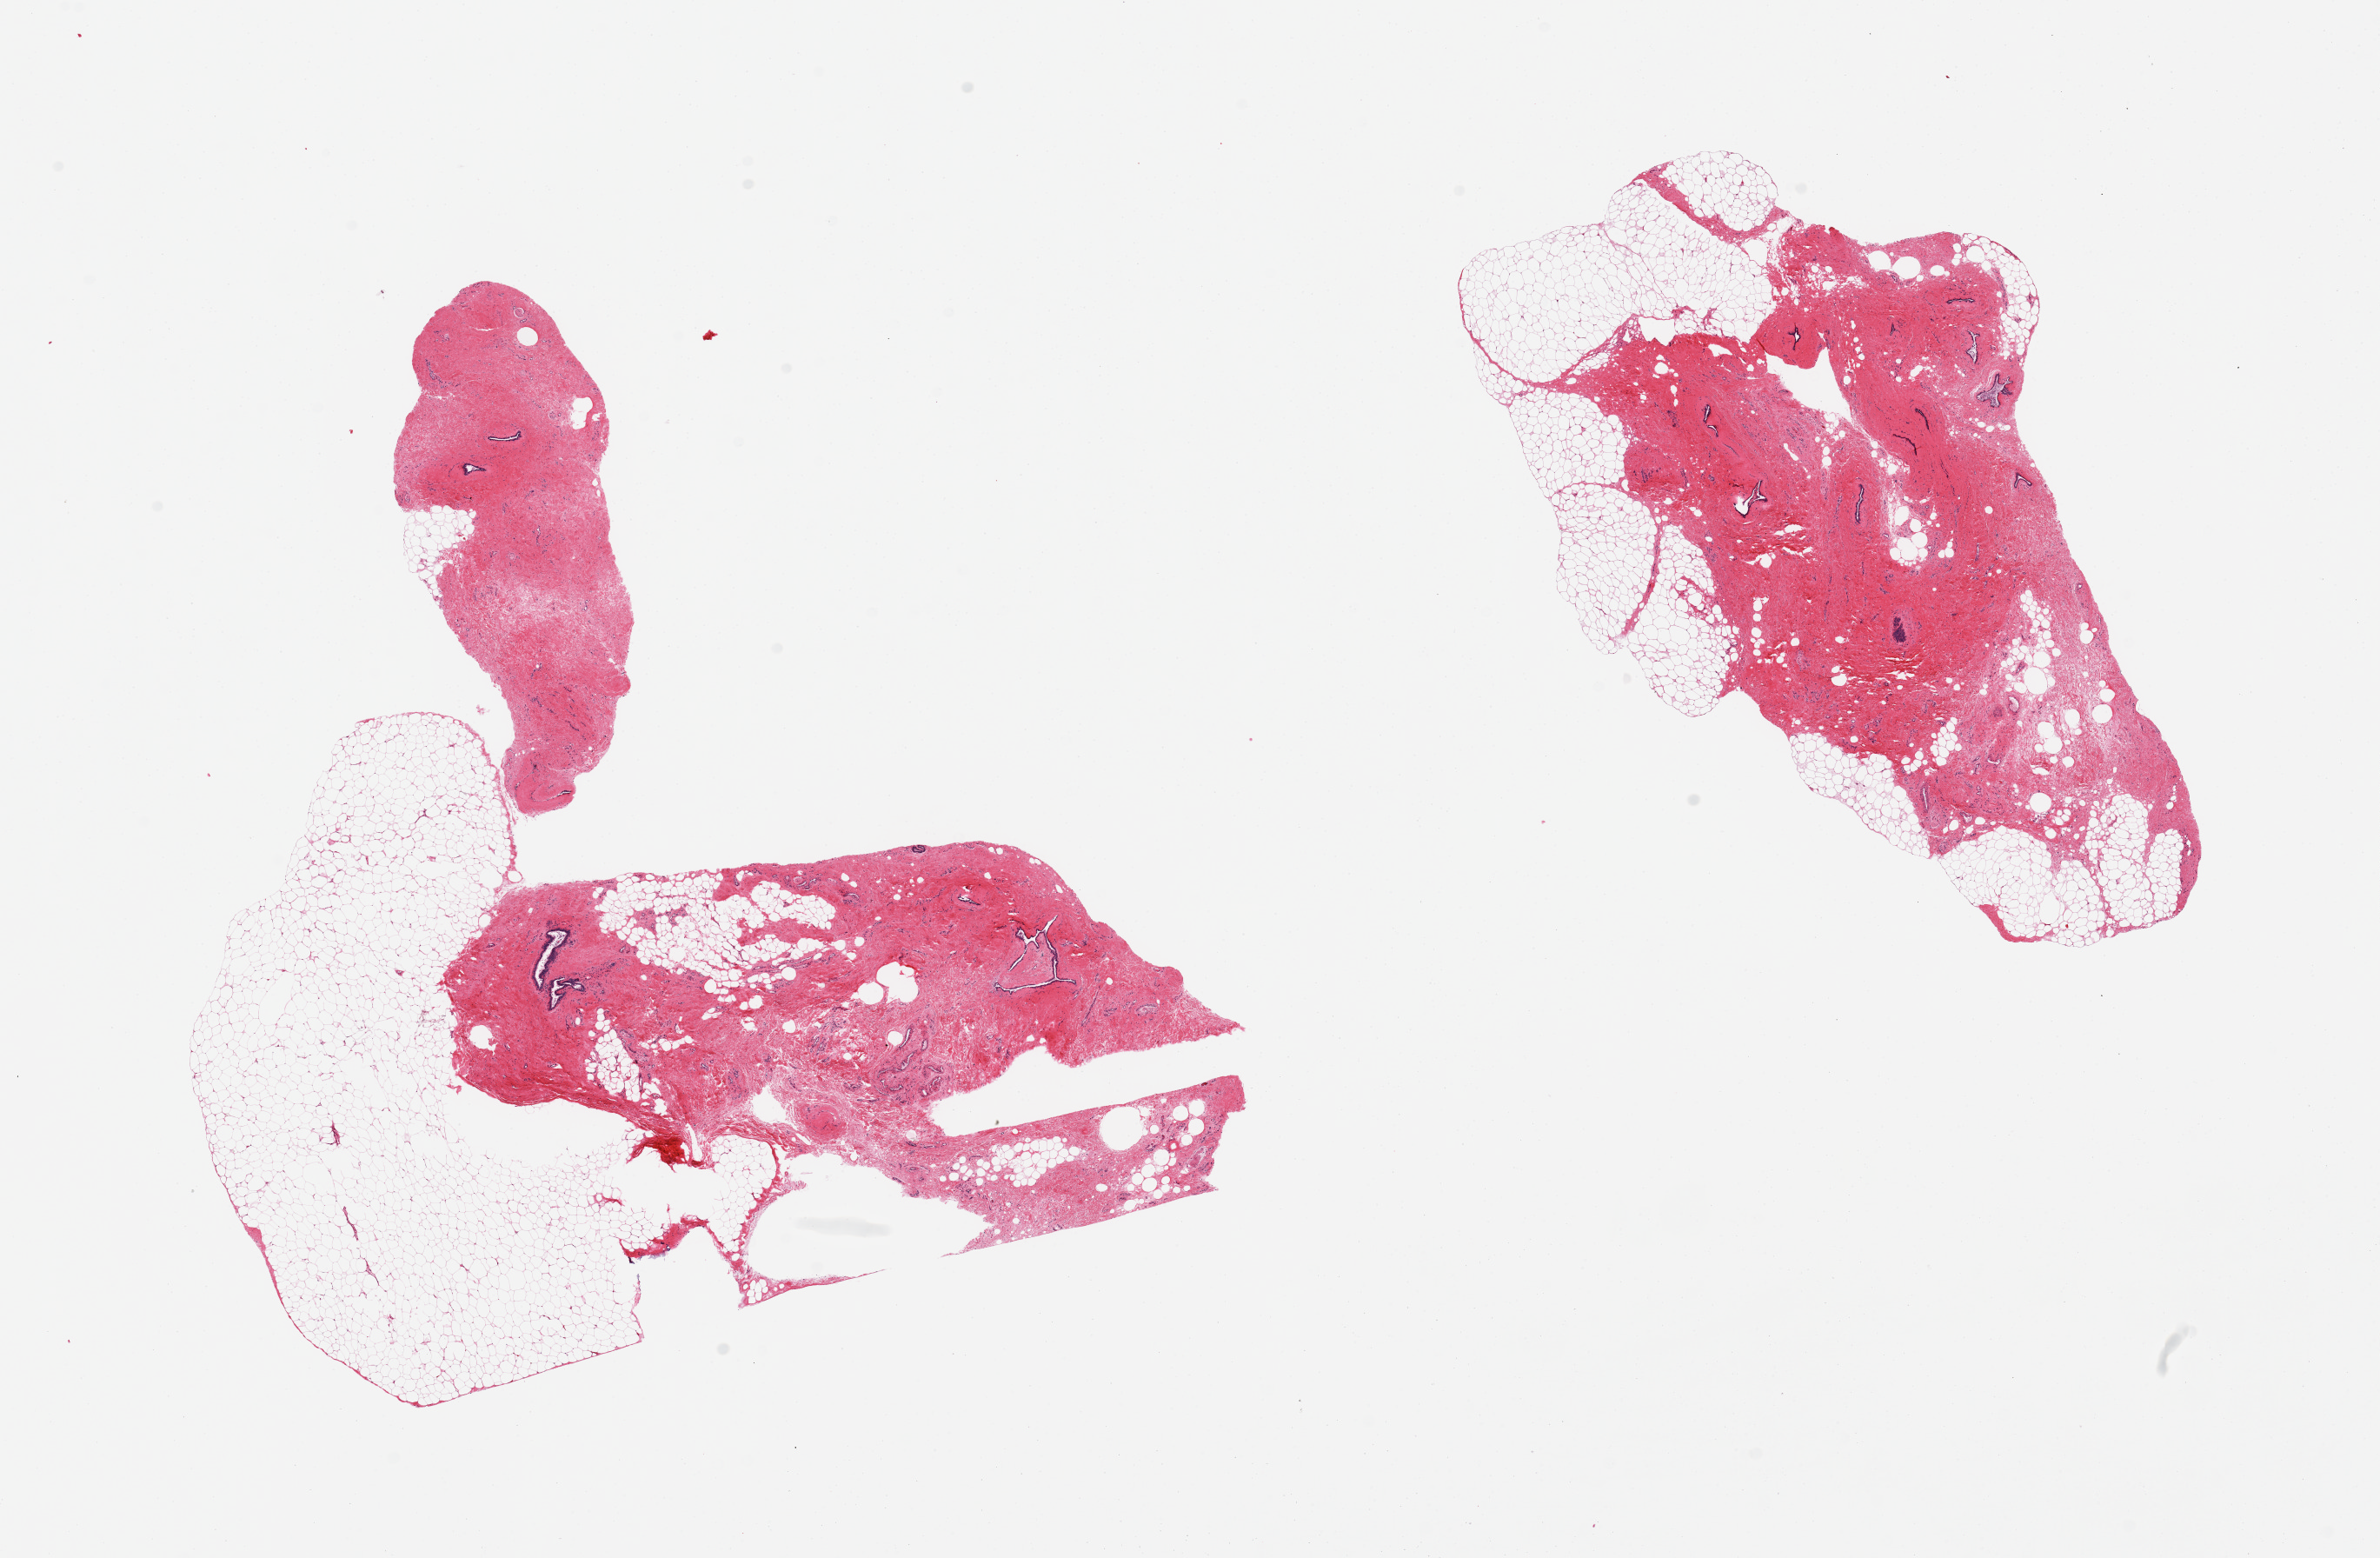
Whole-slide image, hematoxylin and eosin (H&E) stain, brightfield, whole scanned area (about 21.7 x 14.2 mm) shown as a low-resolution overview; PAXgene-fixed, paraffin-embedded tissue; target tissue: breast; donor tissue sample. Donor: male.
Pathologist's review note for this sample: 2 pieces, 50-75% fibrous tissue and ducts with gynecomastoid change.